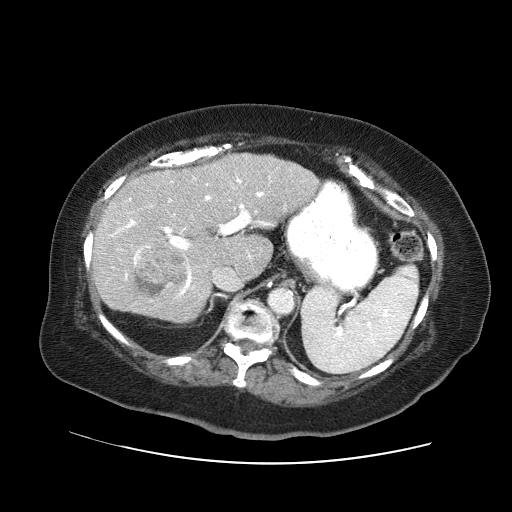
Contrast-enhanced abdominal CT (liver protocol), one axial slice. Slice 35 of 71 in the series (ordered by position). Reconstruction kernel STANDARD. Soft-tissue window (W 400 / L 40 HU). 512 × 512 image matrix. Case-level facts recorded for this patient, not image findings: diagnosis: hepatocellular carcinoma (patient treated with transarterial chemoembolisation; whether this scan precedes or follows treatment is not stated here); TNM stage (as recorded): Stage-II; Child-Pugh class: A; tumour differentiation: poorly differentiated; tumour nodularity: multinodular.
Structures marked on this image (semi-automatic segmentation, software-assisted and operator-edited):
- liver parenchyma outside the tumour (the mass and vessels are separate outlines, so this box may not span the whole liver): box from (x=92, y=153) to (x=318, y=322) px
- mass: (x=134, y=240)–(x=188, y=296)
- liver vessels: (x=110, y=177)–(x=270, y=298)